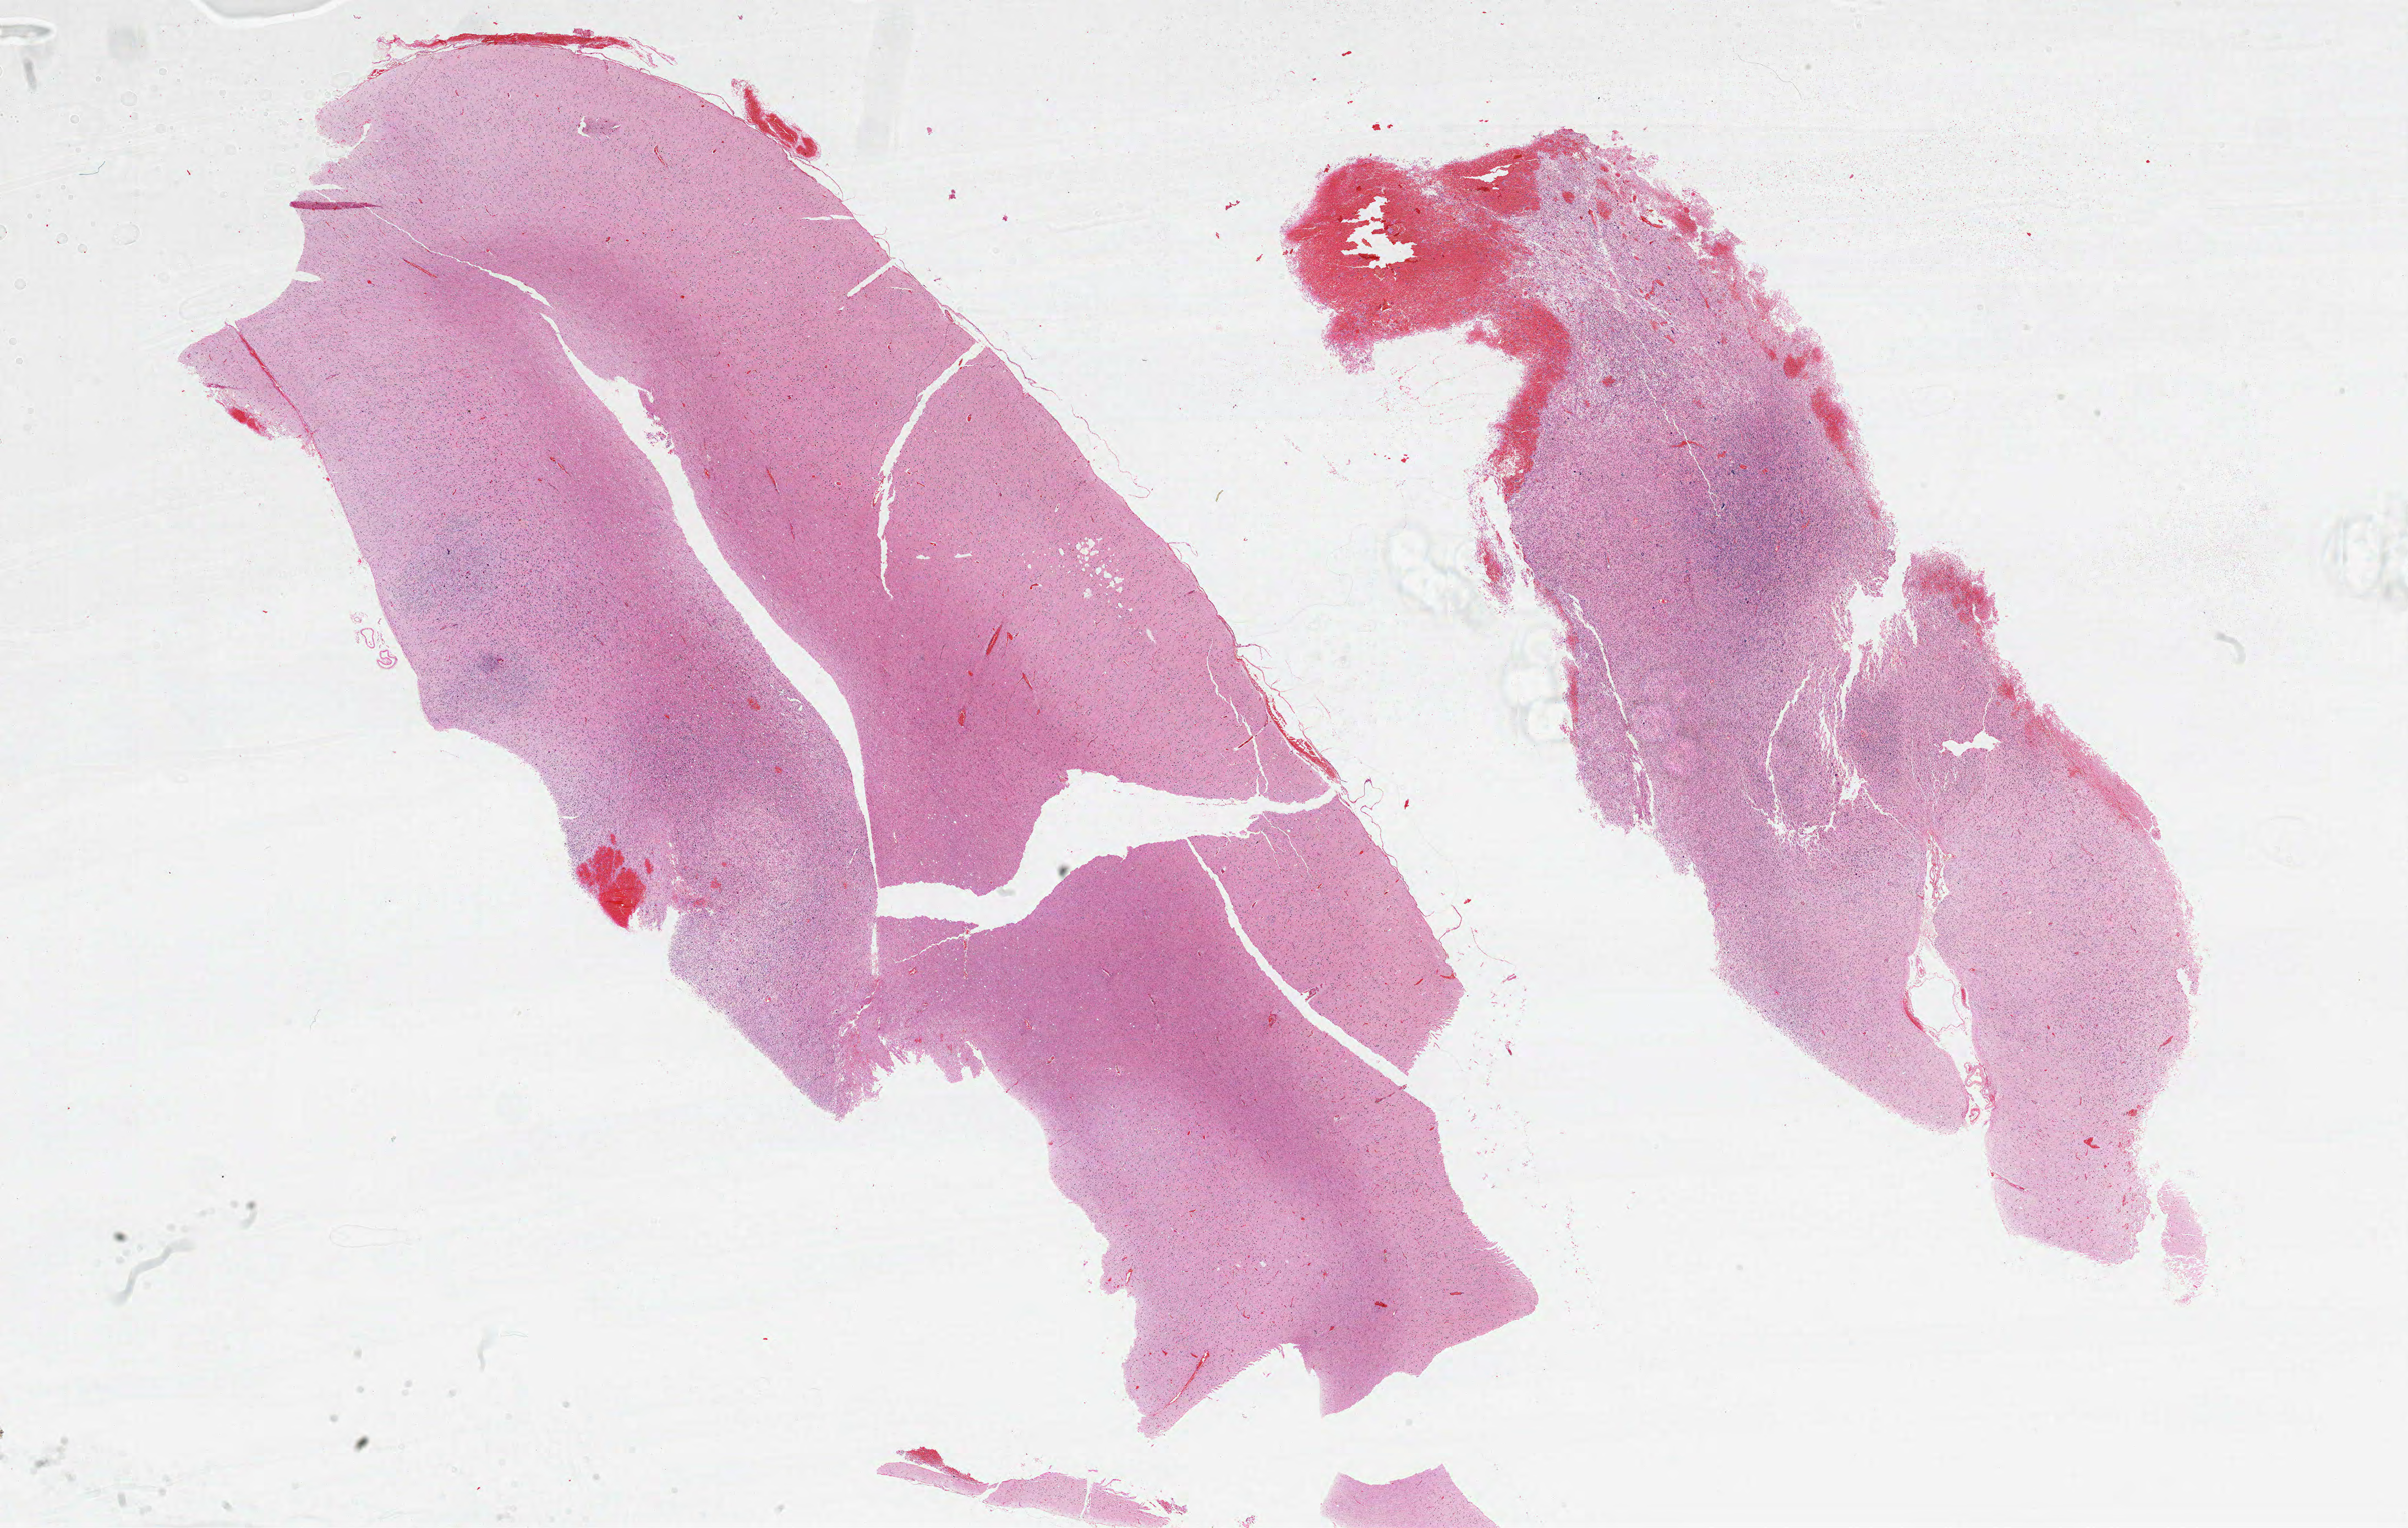
Digitized Hematoxylin and eosin (H&E) stained tissue section (whole slide) — shown as a low-resolution overview of the whole scanned area (about 35.0 x 22.2 mm). Formalin-fixed paraffin-embedded (FFPE) diagnostic section. Brain, primary tumour sample. Patient: male, age at initial diagnosis 51 years.
Pathologic diagnosis: Glioblastoma.